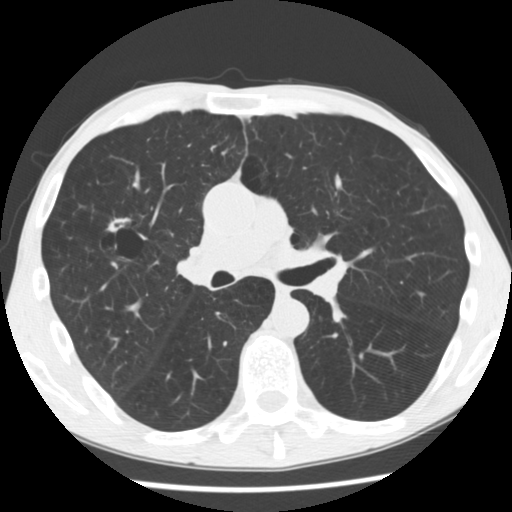
Chest CT (low-dose screening protocol), one axial image, first (baseline) screen, lung window (W 1500 / L -600 HU), standard (soft-tissue) reconstruction kernel (STANDARD), 120 kVp, slice 128 of 292 in the series. Male, age 56 years at enrolment. Current smoker at enrolment.
Lesion marked by an expert reader, bounding box <97,206,154,255> (left, top, right, bottom; pixels). The screening reader recorded 2 non-calcified nodules or masses ≥4 mm on this exam; which of them this box marks is not recorded. Participant outcome: lung cancer diagnosed 476 days after this screen — squamous cell carcinoma, NOS, right upper lobe, right middle lobe, well differentiated (G1), stage IA (AJCC 6th edition), 27 mm at pathology.